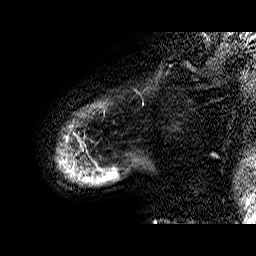
Breast MRI (dynamic contrast-enhanced), one sagittal slice; position 2 of 60 along the scan axis; dynamic contrast-enhanced series, time point 2 of 6 at this slice position (early post-contrast); 1.5 T; TE 6.4 ms, TR 32.9 ms; 4 mm slice thickness; 256 × 256 image matrix, field of view 200 × 200 mm. Female patient. Case-level facts recorded for this patient, not image findings: setting: breast cancer imaged before/during neoadjuvant chemotherapy; receptor status: HR-positive, HER2-negative.
Annotated regions visible in this slice (semi-automatically segmented with operator editing):
- analysis volume of interest (the breast-tissue region the enhancement analysis was run in; not a lesion): bounding box <57,101,143,187> (left, top, right, bottom; pixels)
- tumour enhancement mask (voxels above the 100 % enhancement threshold inside the analysis volume of interest): <60,159,74,175>